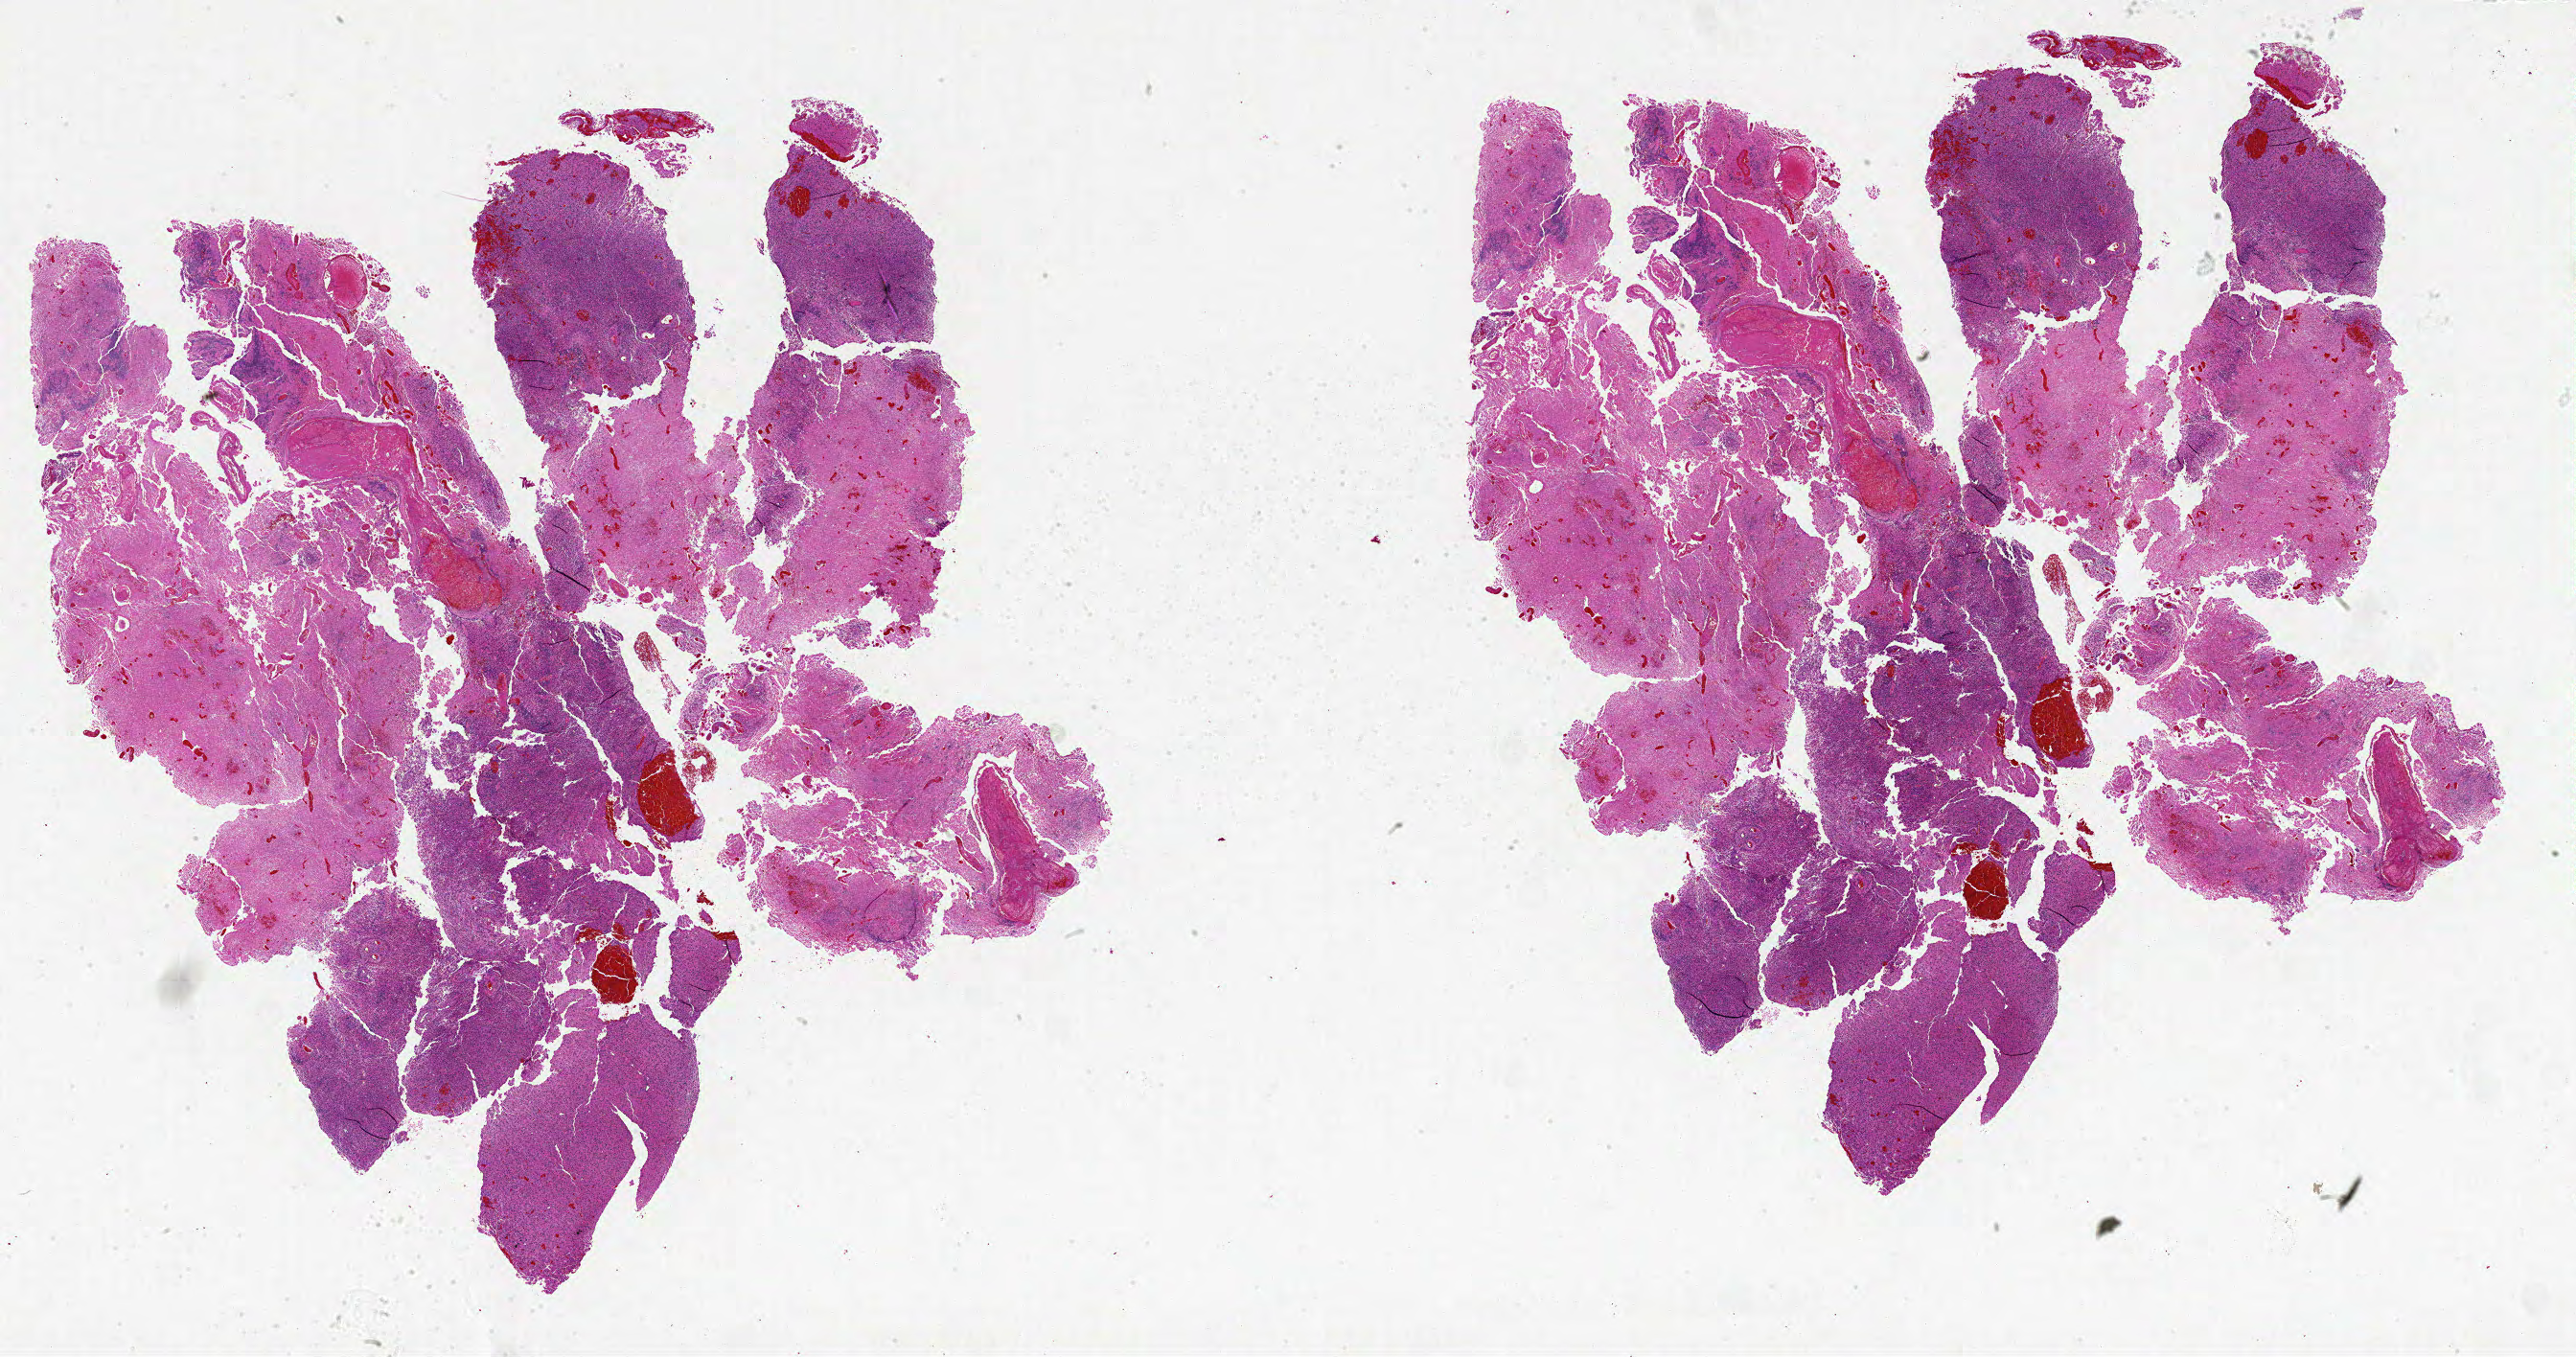
H&E-stained whole-slide image — low-resolution overview of the scanned area, about 43.0 x 22.6 mm (acquisition: 20x scan); FFPE section; primary tumour sample from the brain. Patient: male, age at initial diagnosis 77 years.
Diagnosis: Glioblastoma.